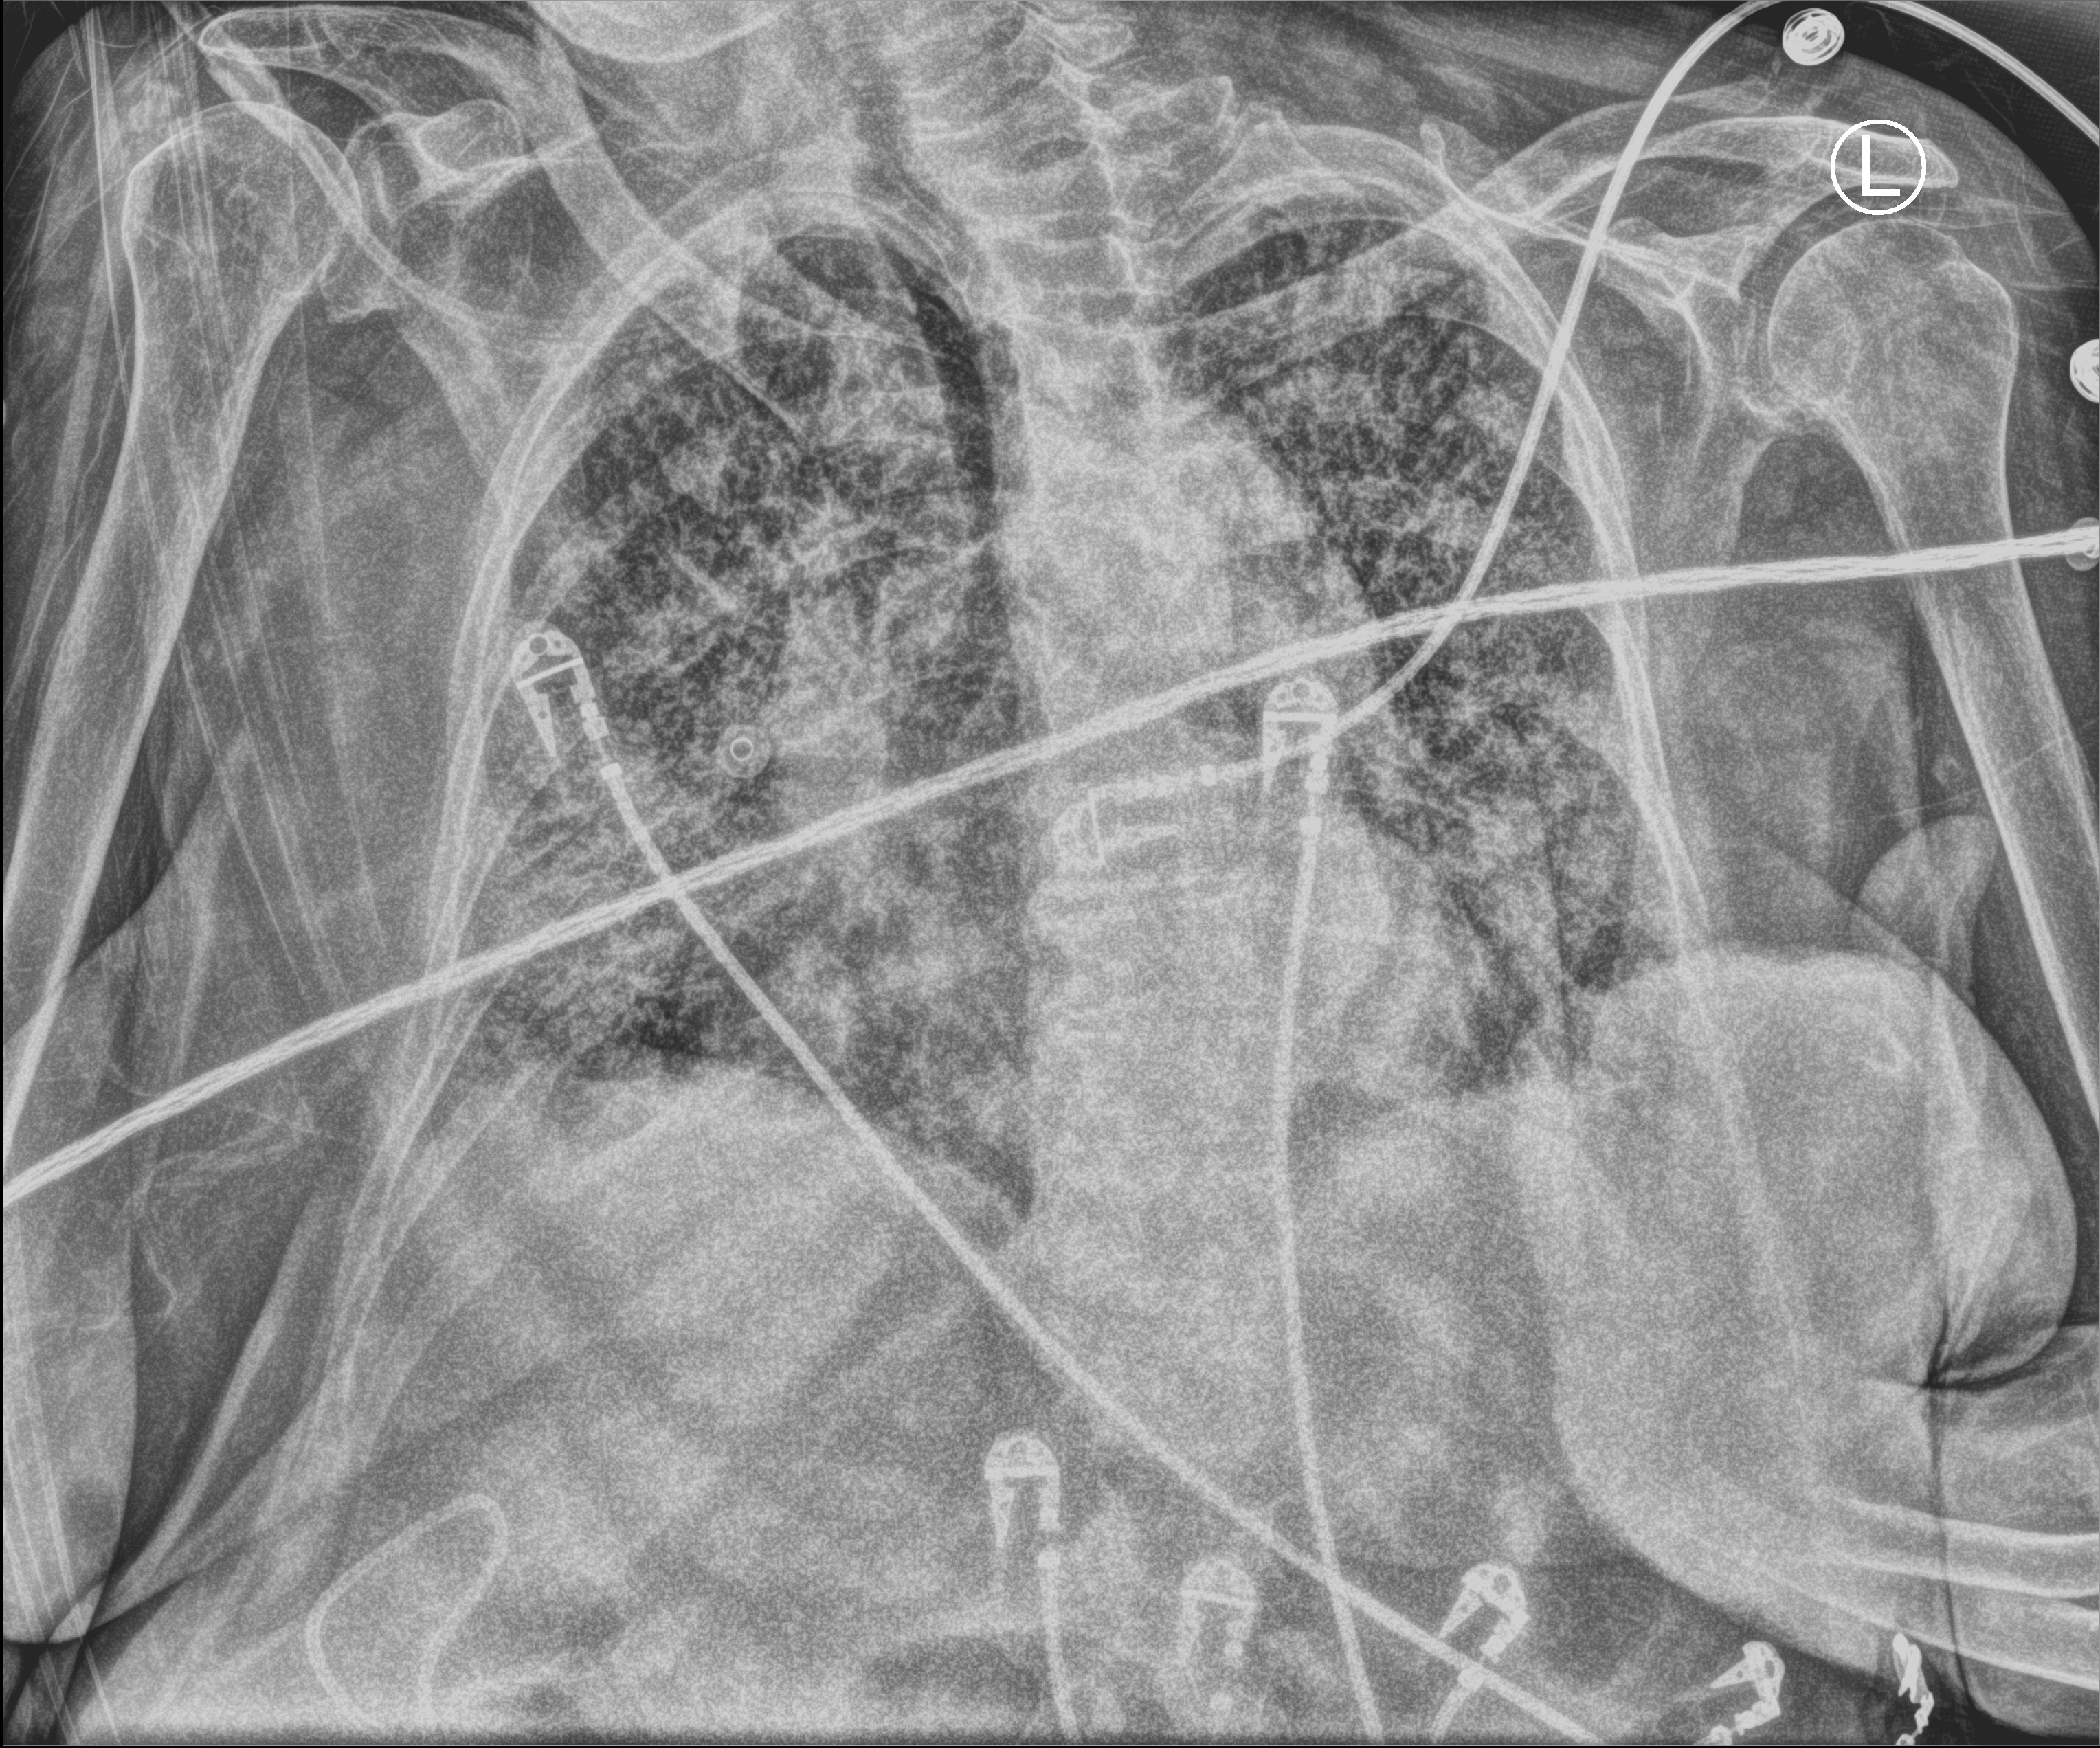
Bedside chest radiograph (computed radiography), anteroposterior (AP) projection. Patient hospitalised with COVID-19; female, aged 75–90 years.
Admission-level facts for this patient (not findings on this image; timing relative to this image not recorded): length of hospital stay: 17 days.